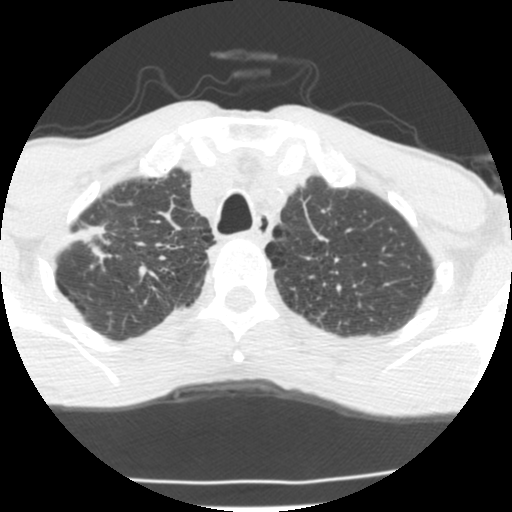
Low-dose screening chest CT, one axial slice. Position 178 of 214 along the scan axis. Lung window (W 1500 / L -600 HU). 2.5 mm slice thickness. 512 × 512 image matrix.
Structures marked on this image (manually delineated by an expert):
- lesion 1 (tumor, upper lobe of right lung): bounding box <71,224,106,244> (left, top, right, bottom; pixels)